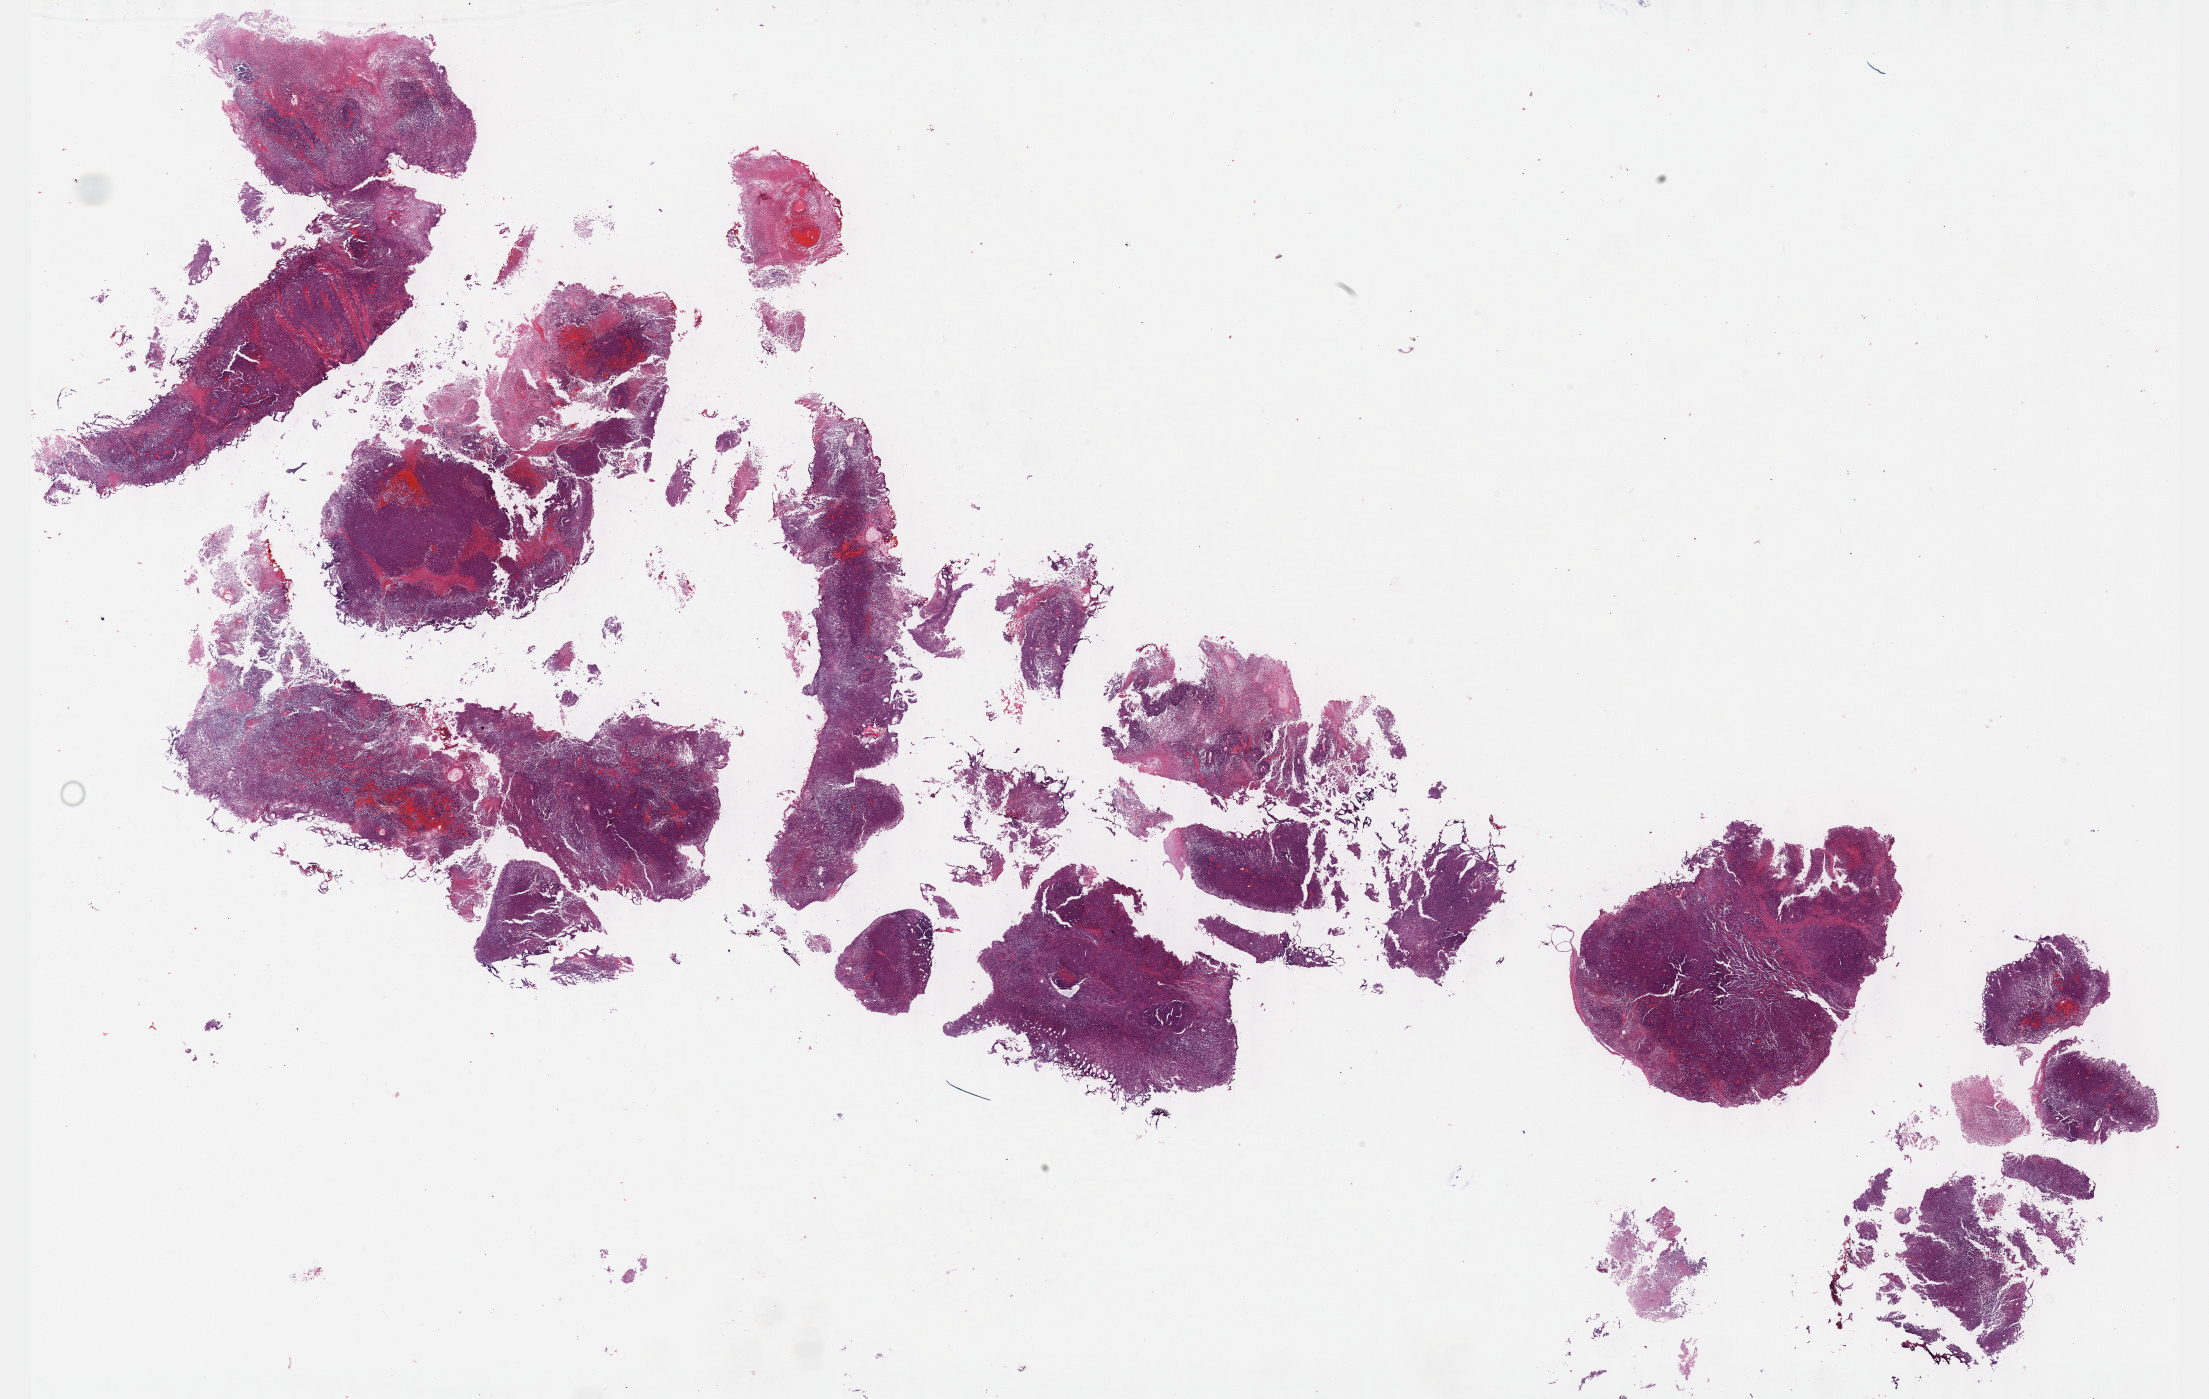
Digitized Hematoxylin and eosin (H&E) stained tissue section (whole slide) — whole scanned area (about 35.7 x 22.6 mm) shown as a low-resolution overview; formalin-fixed paraffin-embedded (FFPE) diagnostic section; primary tumour sample from the bladder. Male, age 49 years at initial diagnosis. Histologic grade: high grade.
Pathologic diagnosis: Transitional cell carcinoma. TNM: T3b NX MX. AJCC pathologic stage: III (7th edition).